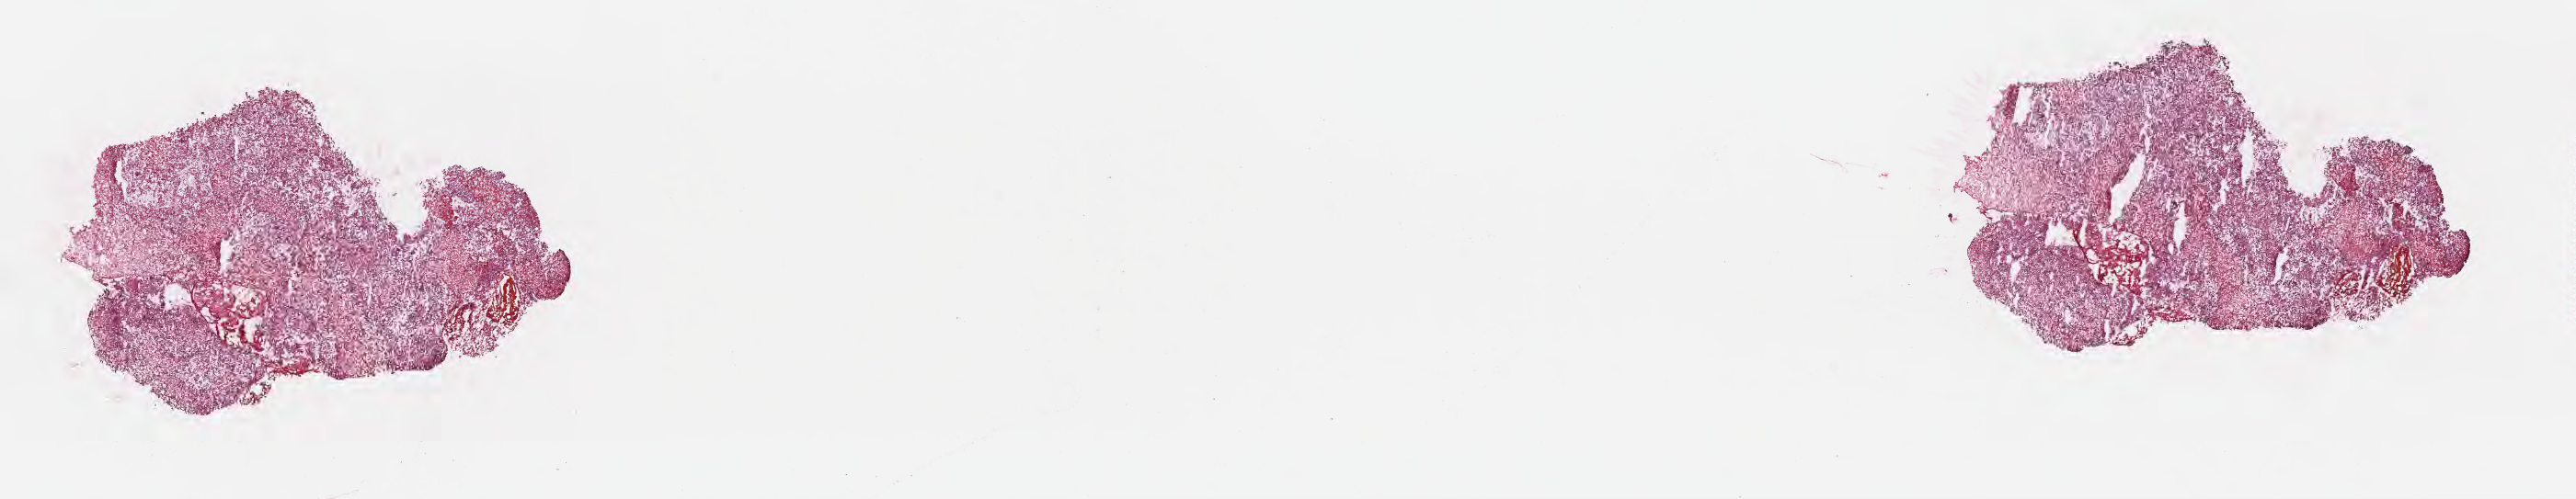
Whole-slide image, H&E stain, low-resolution overview of the scanned area, about 22.7 x 4.4 mm. Frozen section (tissue freezing medium). Metastatic tumor tissue, resected from brain. Male, age 73 years at initial diagnosis. Composition of this section per pathologist review: tumor cells 40%, tumor nuclei 50%, stromal cells 40%, necrosis 20%, normal cells 0%. Inflammatory infiltration, as recorded: lymphocyte infiltration 0%, monocyte infiltration 0%, neutrophil infiltration 0%.
Section: bottom of the tissue portion. Patient diagnosis (primary): Malignant melanoma, NOS.